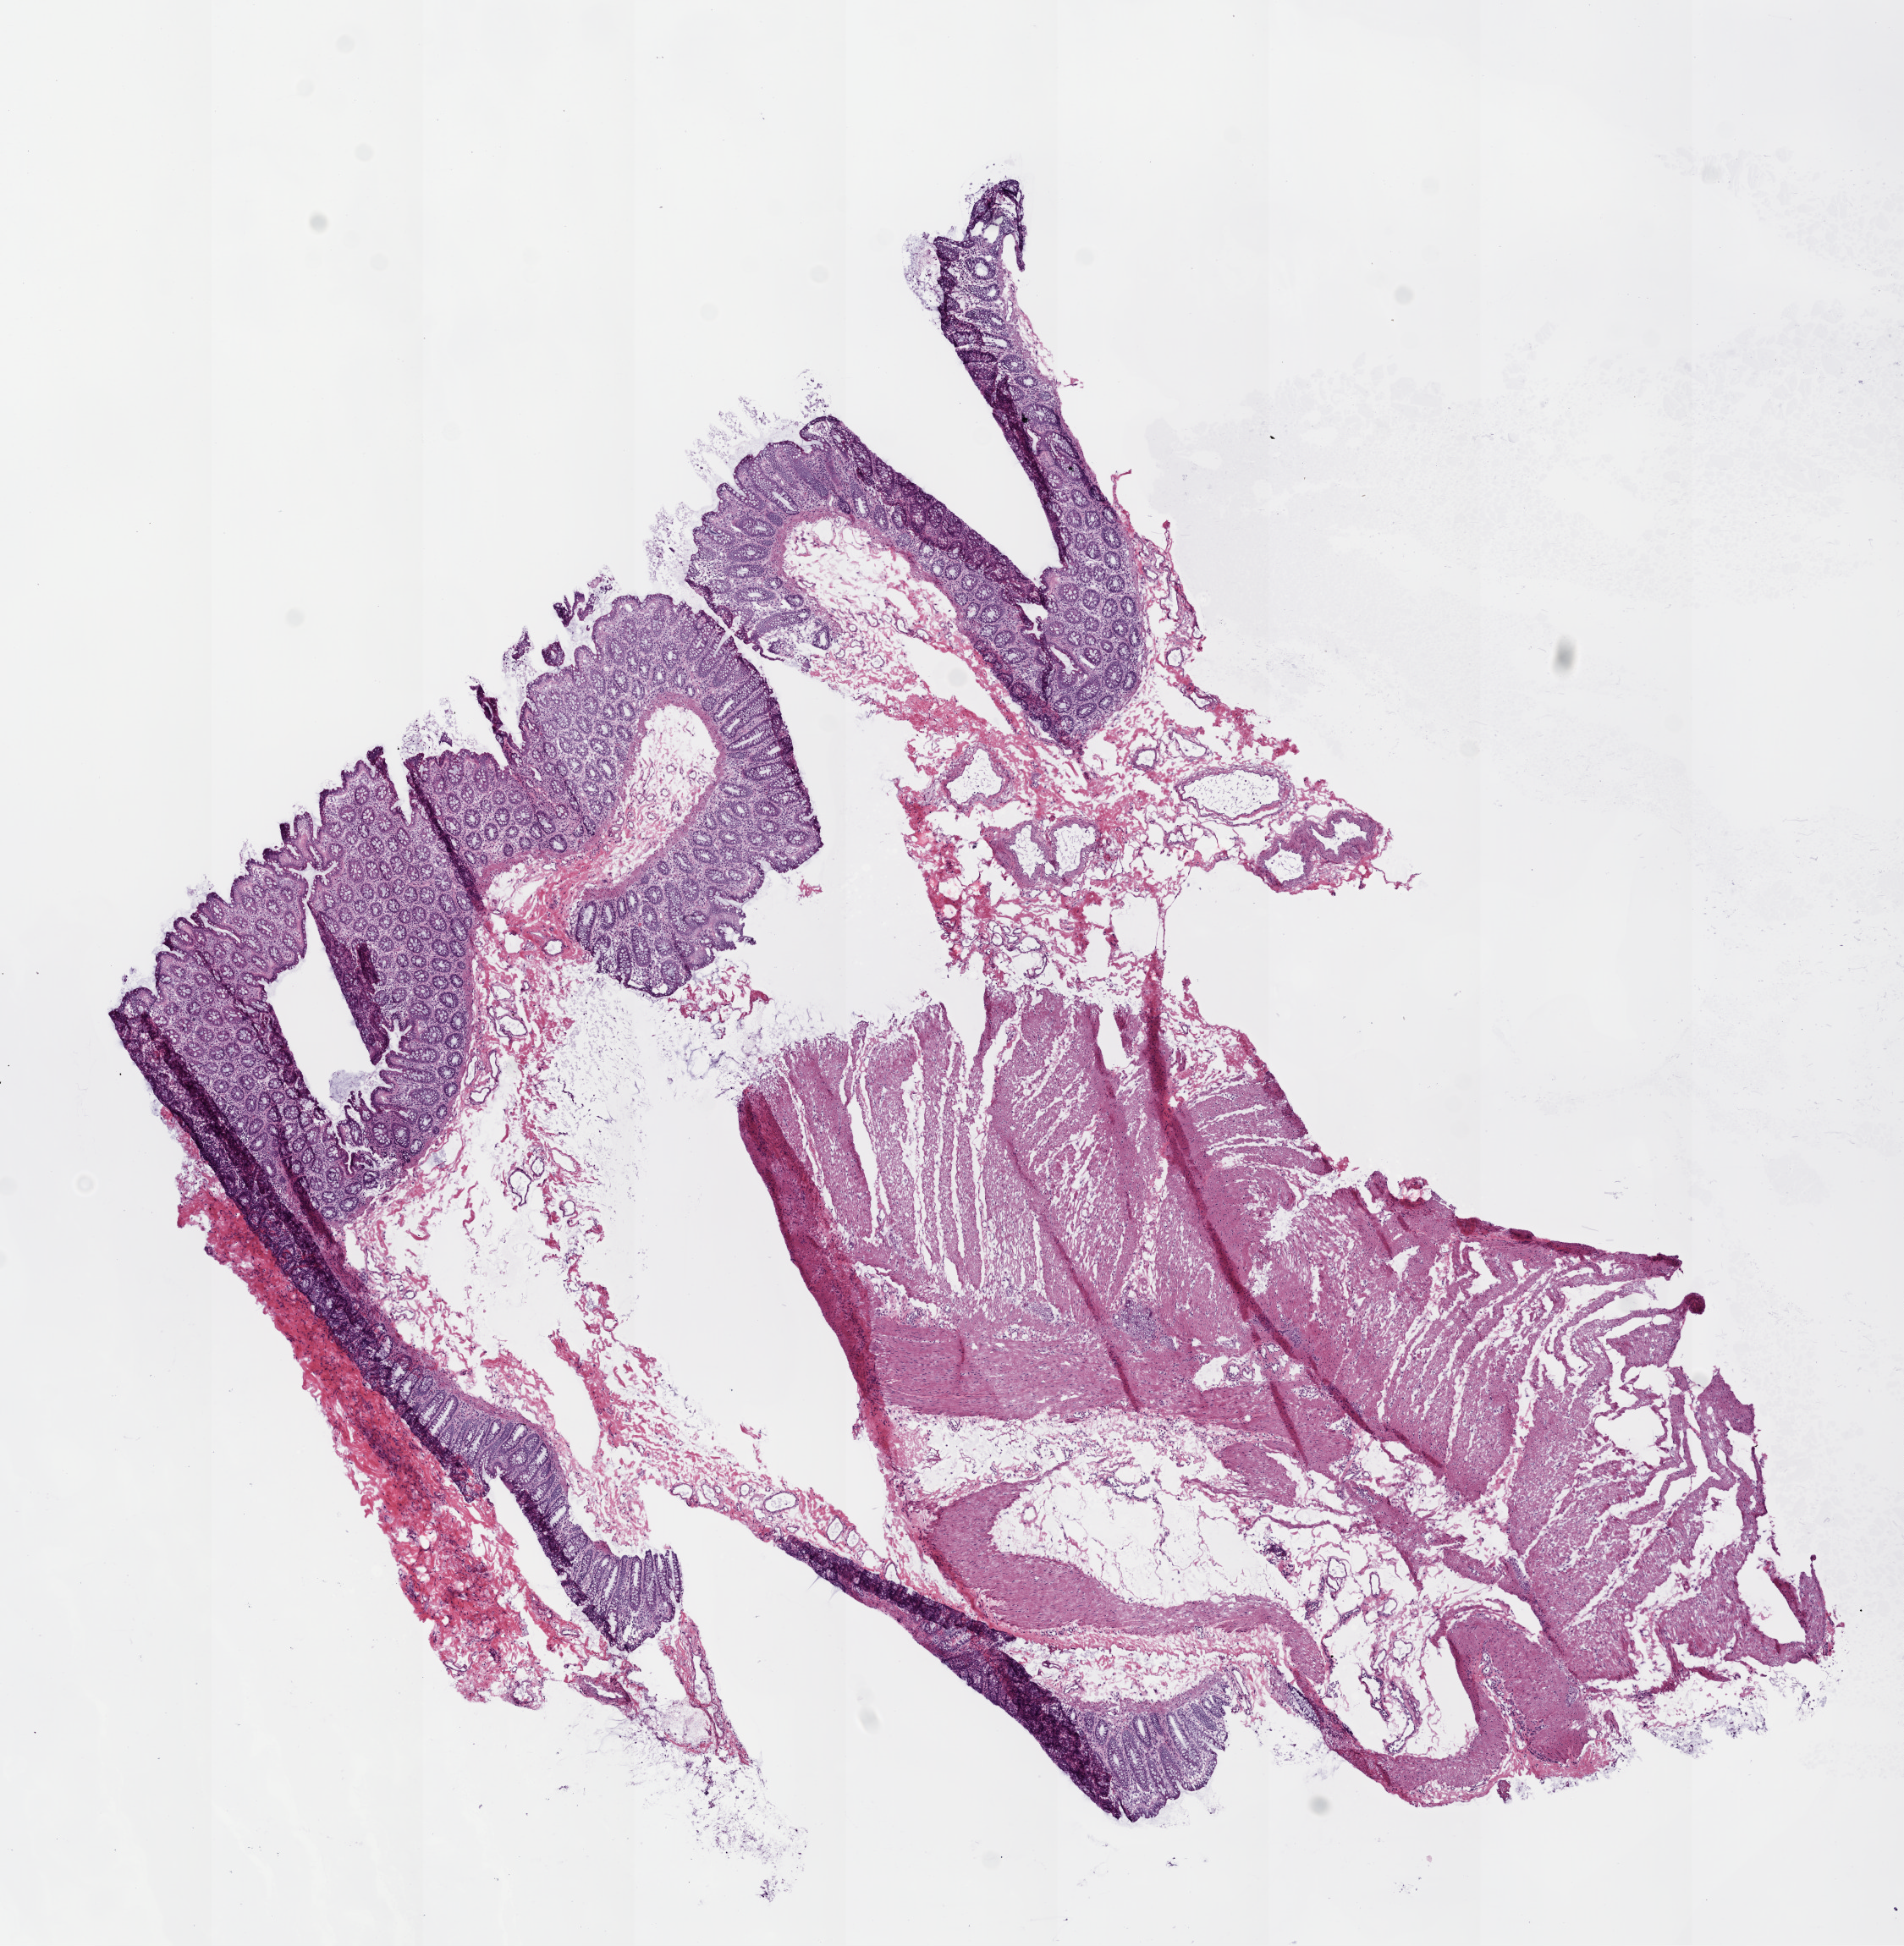
Whole-slide histology image, H&E — whole scanned area (about 9.0 x 9.2 mm, acquisition: 20x scan) shown as a low-resolution overview, frozen section, solid tissue normal (non-tumour tissue) sample from the colon. Female patient; age at initial diagnosis 82 years.
This section: solid tissue normal (non-tumour) sample from the same patient. Patient diagnosis: Adenocarcinoma, NOS (ascending colon).